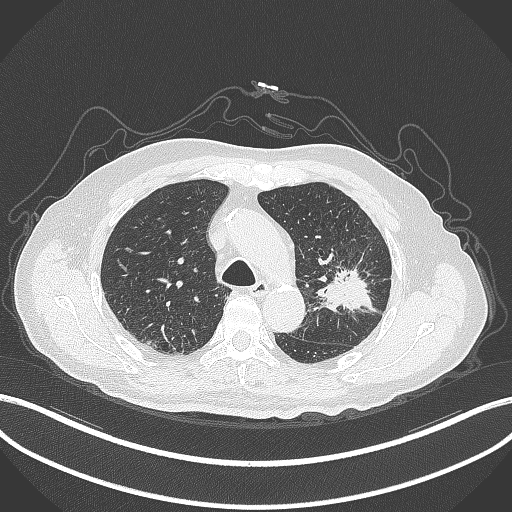
Chest CT, one axial slice. Slice 208 of 331 in the series (ordered by position). Reconstruction kernel B70f. 120 kVp. Lung window (W 1500 / L -600 HU). 1 mm slice thickness. 512 × 512 image matrix. Male patient, age 79 years. Case-level facts recorded for this patient, not image findings: clinical TNM (as recorded): T2a N1 M1; histopathological grade: G3.
Annotated regions visible in this slice (bounding box drawn by a radiologist):
- lung tumour (recorded histology: adenocarcinoma): box from (x=311, y=261) to (x=383, y=320) px